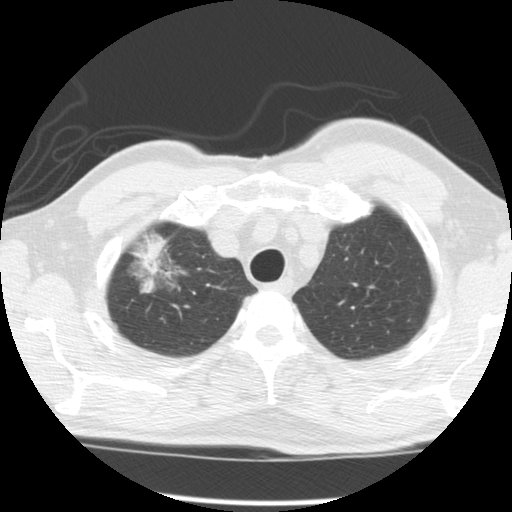
Chest CT (low-dose screening protocol), one axial image, second screening round (one year after baseline), lung window (W 1500 / L -600 HU), 2.5 mm slice thickness, standard (soft-tissue) reconstruction kernel (STANDARD), 120 kVp. Male participant, aged 64 years at enrolment. Former smoker at enrolment.
• Expert-annotated lung lesion, bounding box (x1, y1, x2, y2) in pixels: (121, 233, 191, 303).
• The screening reader recorded 2 non-calcified nodules or masses ≥4 mm on this exam; which of them this box marks is not recorded.
• Official screen result: positive, other.
• Participant outcome: lung cancer diagnosed 429 days after this screen (after the third annual screen) — adenocarcinoma, NOS, right upper lobe, well differentiated (G1), stage IB (AJCC 6th edition), 45 mm at pathology.